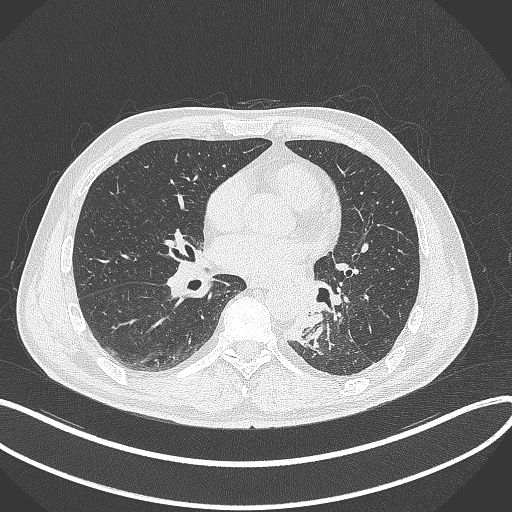
Chest CT, one axial slice; slice 150 of 329 in the series (ordered by position); reconstruction kernel B70f; 120 kVp; lung window (W 1500 / L -600 HU); 1 mm slice thickness; 512 × 512 image matrix, field of view 400 × 400 mm. Patient: male, 59 years. From the clinical record (not read from this slice): clinical TNM (as recorded): T2a N2 M0.
Annotated regions visible in this slice (rectangle marked by the reading radiologist):
- lung tumour (recorded histology: squamous cell carcinoma): bounding box <283,291,332,349> (left, top, right, bottom; pixels)